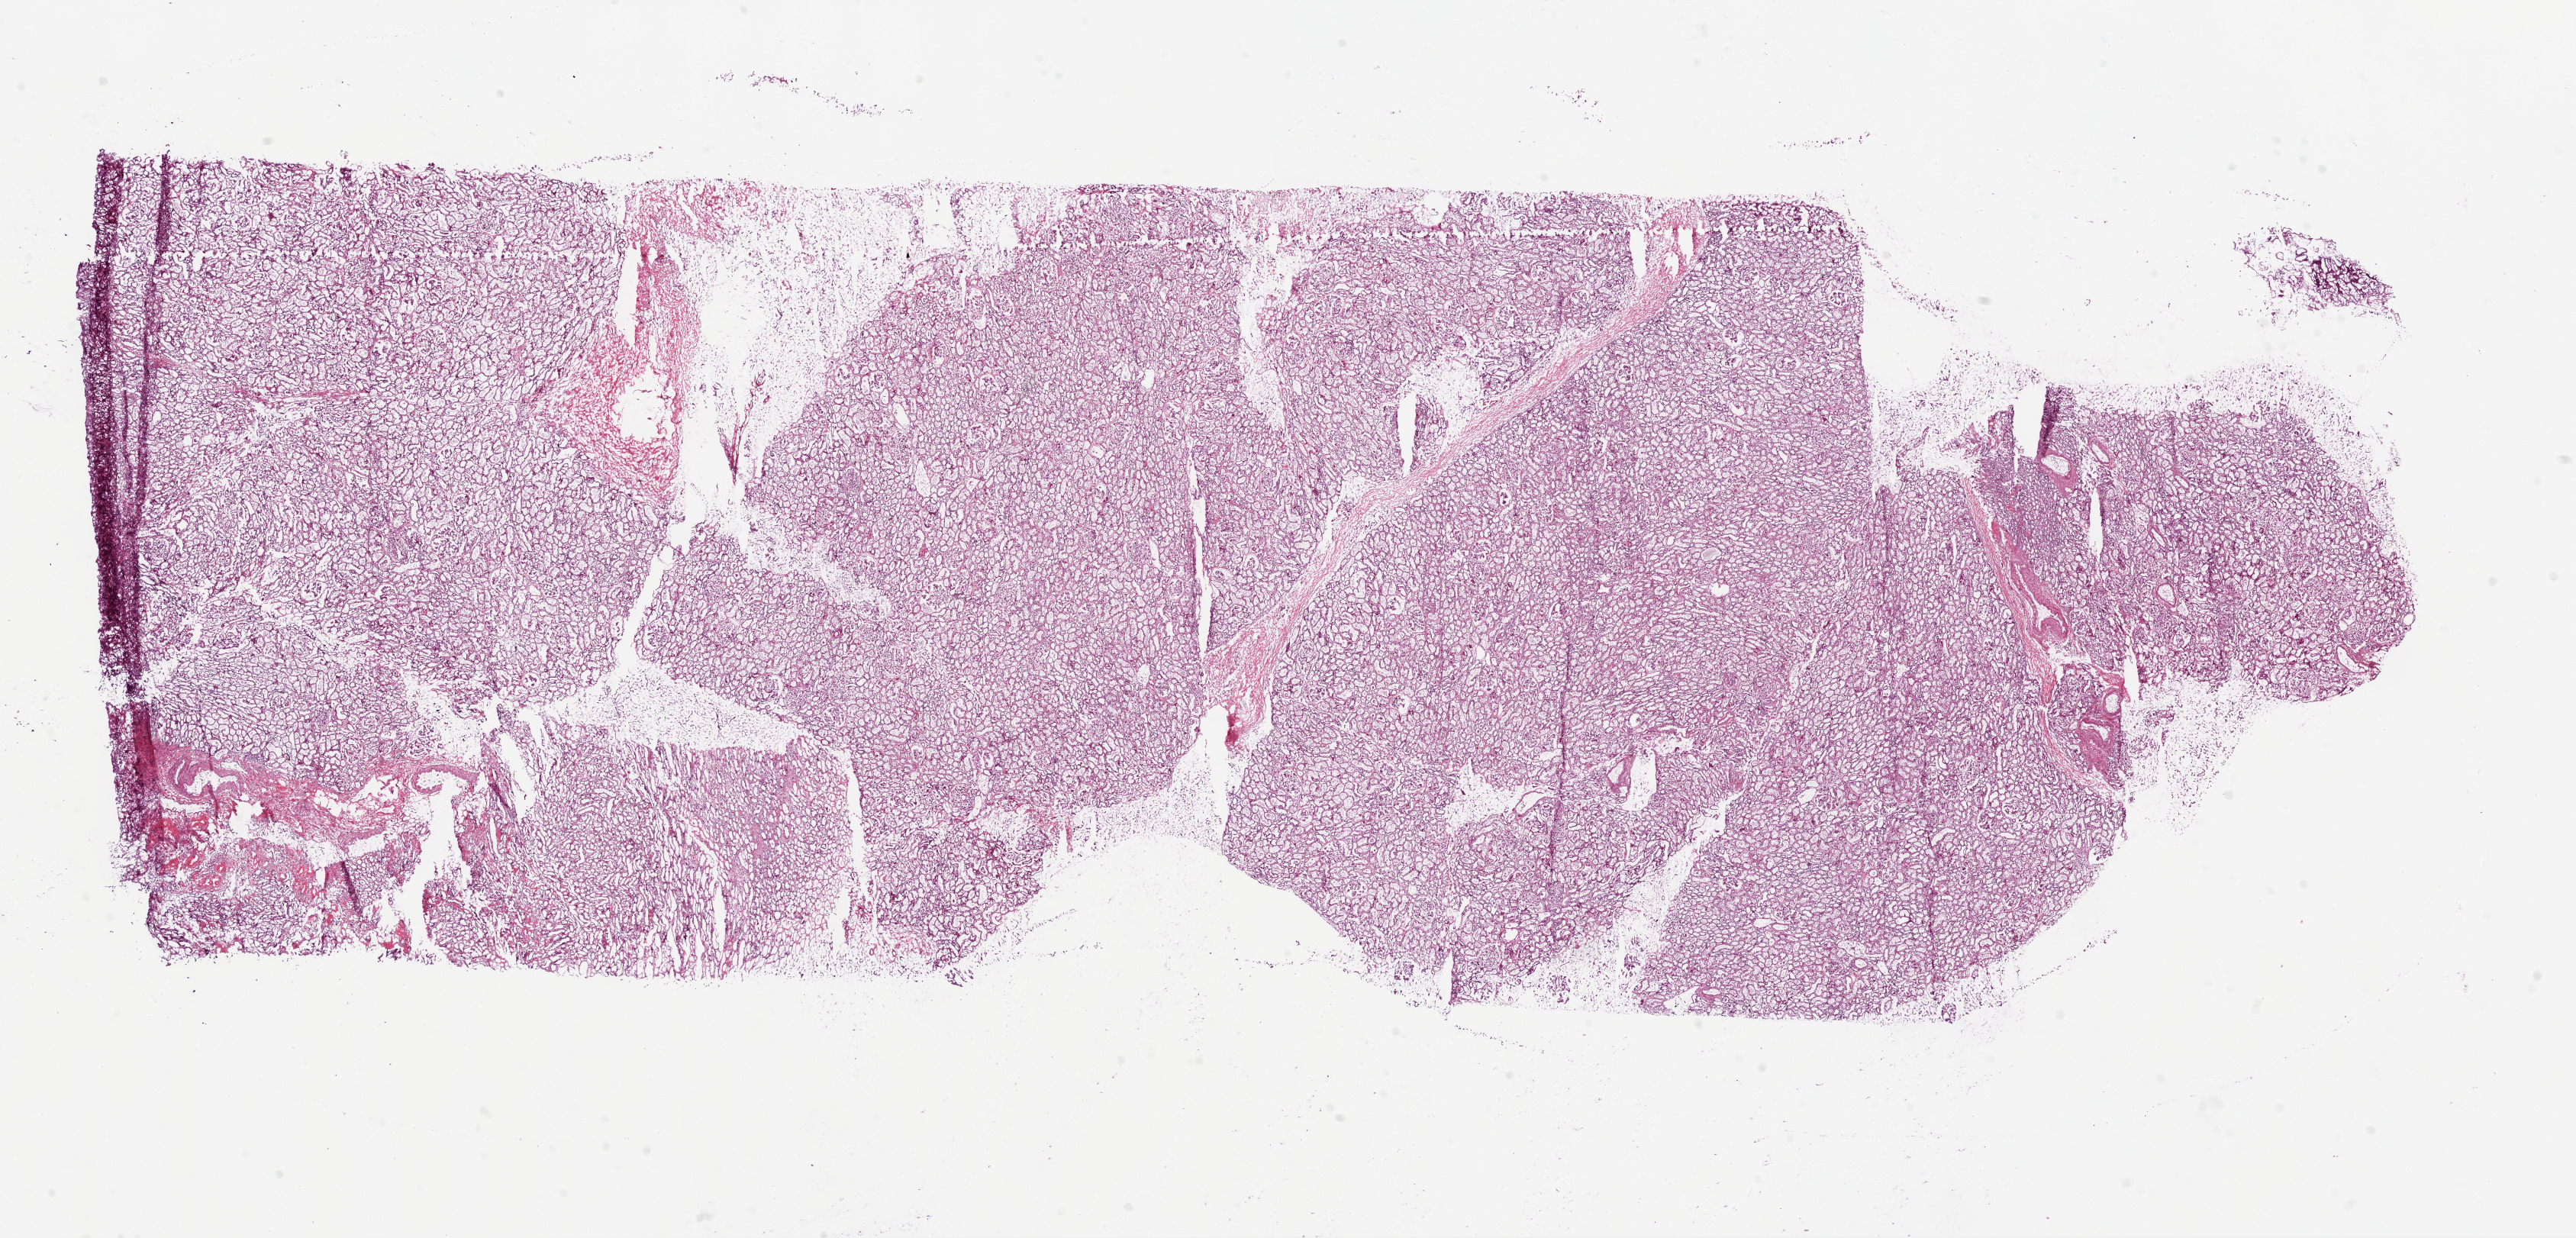
Whole-slide histology image, H&E-stained, whole scanned area (about 27.1 x 13.0 mm) shown as a low-resolution overview, frozen section from the bottom of the tissue portion, kidney, solid tissue normal (non-tumour tissue) sample. Female patient; age at initial diagnosis 52 years.
This section: solid tissue normal sample (biorepository sample class). Patient diagnosis: Clear cell adenocarcinoma, NOS.